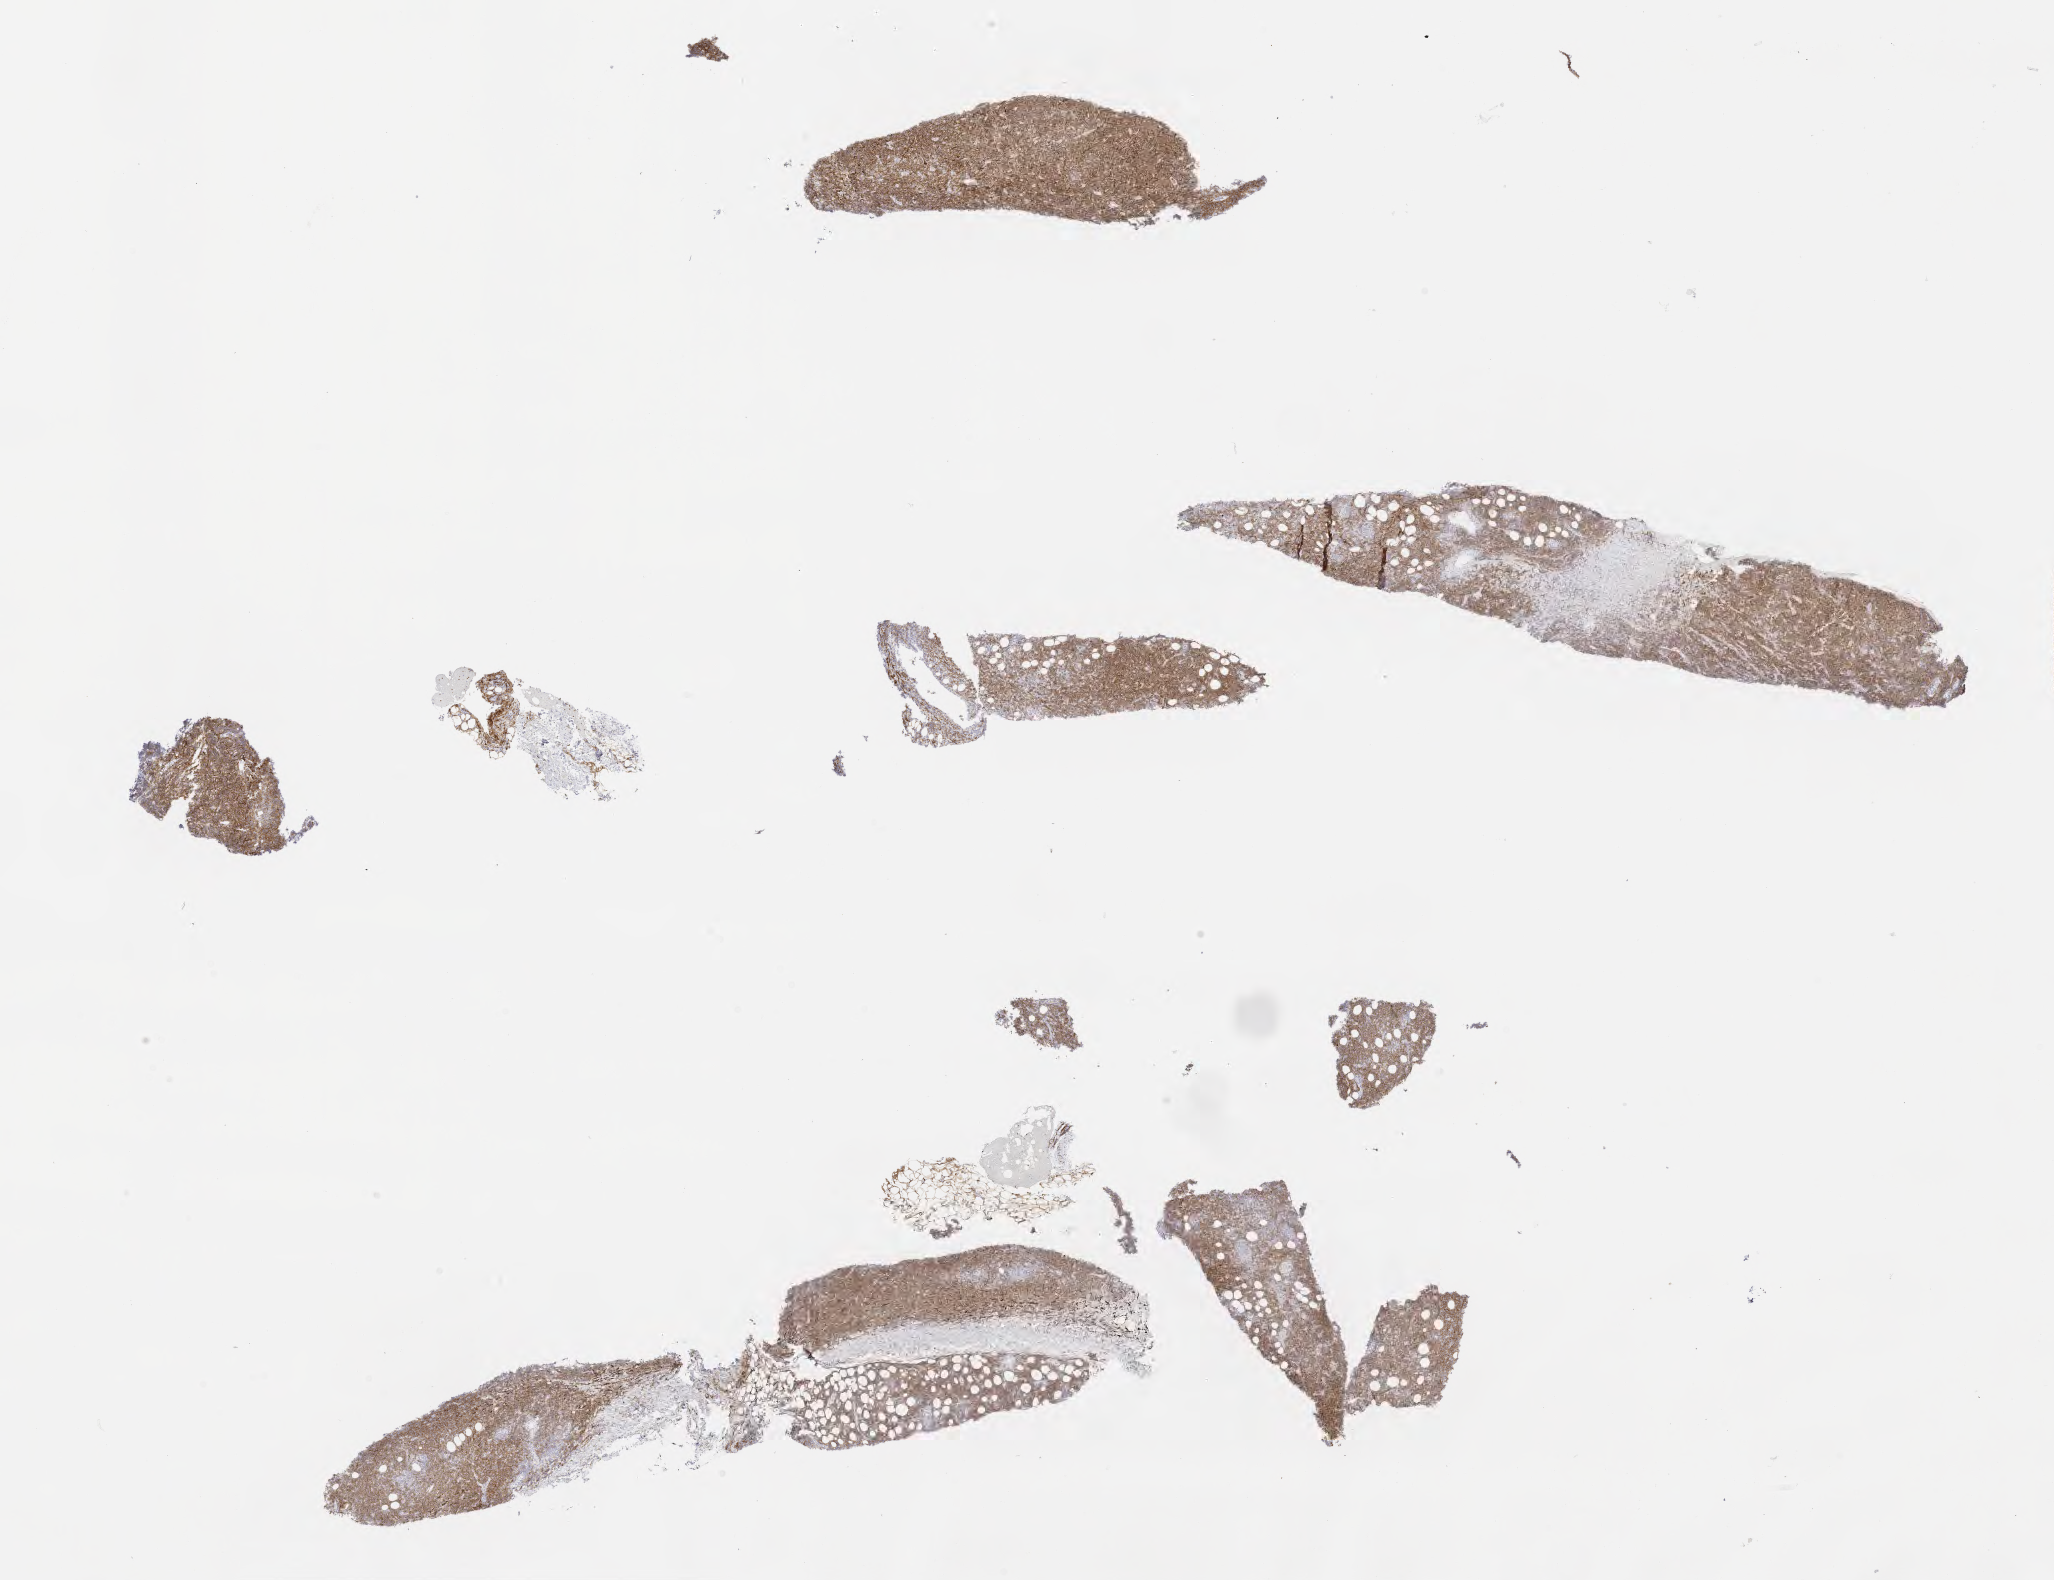
Whole-slide image, immunohistochemical stain for CD10, a low-resolution overview of the entire scanned area, about 16.6 x 12.8 mm. Tumor tissue. Male patient, 33 years old.
Diagnosis: Burkitt lymphoma, NOS.